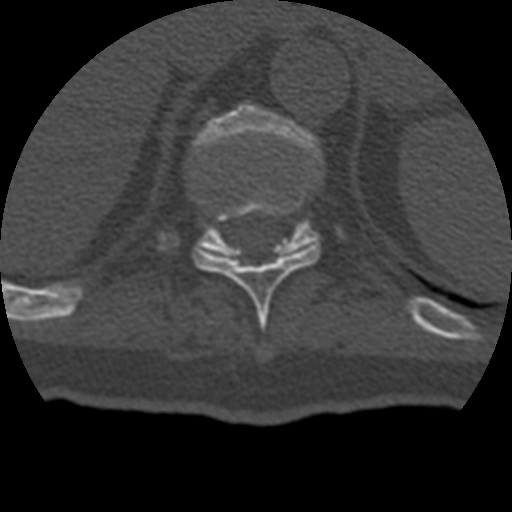
CT including the spine, one axial slice; reconstruction kernel STANDARD; bone window (W 1800 / L 400 HU); 1.25 mm slice thickness; 512 × 512 image matrix, field of view 160 × 160 mm. Patient age 69 years. Case-level facts recorded for this patient, not image findings: primary cancer: prostate.
Outlined on this slice (semi-automatically segmented with operator editing):
- T10 vertebra: box from (x=194, y=206) to (x=320, y=326) px
- T11 vertebra: (x=193, y=104)–(x=321, y=258)